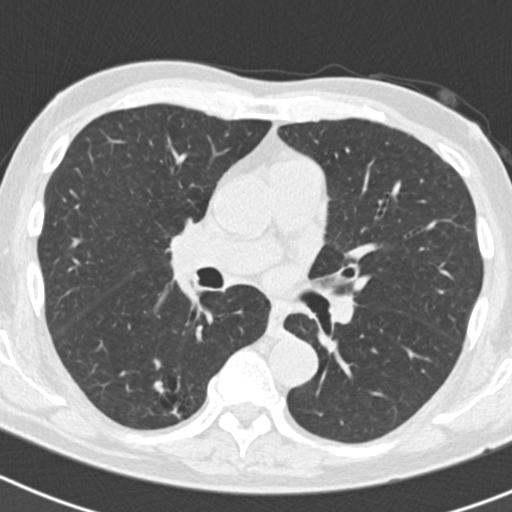
Low-dose screening chest CT, axial slice; second annual screen; lung window (W 1500 / L -600 HU); 2 mm slice thickness; standard (soft-tissue) reconstruction kernel (B30f); 512 × 512 image matrix, field of view 300 × 300 mm. Male, age 70 years at enrolment. Current smoker at enrolment.
Lesion marked by an expert reader, bounding box <131,373,199,433> (left, top, right, bottom; pixels). The screening reader recorded 5 non-calcified nodules or masses ≥4 mm on this exam; which of them this box marks is not recorded.